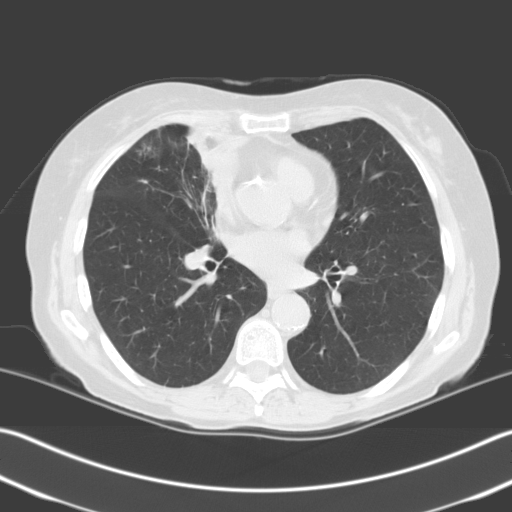
Low-dose screening chest CT, one axial slice; position 110 of 204 along the scan axis; 140 kVp; lung window (W 1500 / L -600 HU); 512 × 512 image matrix, field of view 348 × 348 mm.
Structures marked on this image (expert manual segmentation):
- lesion 1 (tumor, upper lobe of right lung): bounding box [x1, y1, x2, y2] px = [187, 131, 245, 183]